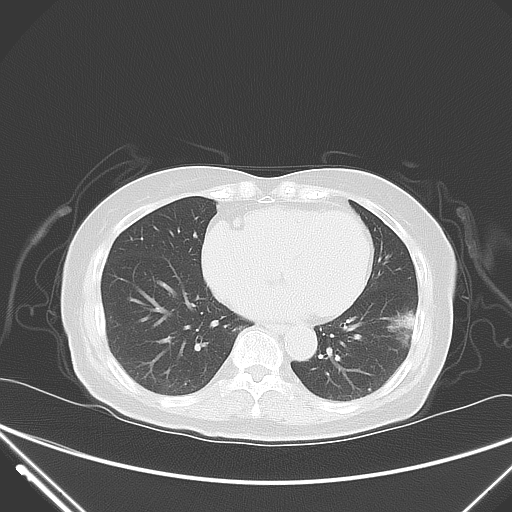
Chest CT, one axial slice. Position 23 of 62 along the scan axis. Lung window (W 1500 / L -600 HU). 5 mm slice thickness. 512 × 512 image matrix, field of view 377 × 377 mm. Patient: female, 82 years. Case-level facts recorded for this patient, not image findings: clinical TNM (as recorded): T1c N0 M0; histopathological grade: G2.
Annotated regions visible in this slice (rectangle marked by the reading radiologist):
- lung tumour (recorded histology: adenocarcinoma): bounding box (x1, y1, x2, y2) in pixels: (383, 308, 421, 355)